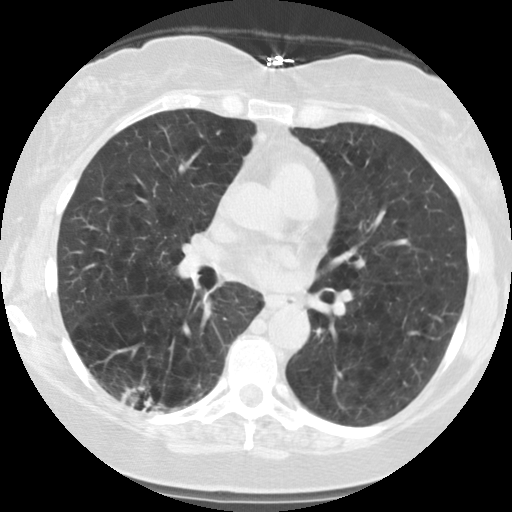
Chest CT (low-dose screening protocol), one axial image. Second annual screen. Lung window (W 1500 / L -600 HU). 2.5 mm slice thickness. Female, age 59 years at enrolment. Current smoker at enrolment.
Expert-annotated lung lesion, bounding box [x1, y1, x2, y2] px = [106, 362, 185, 426]. The screening reader recorded 2 non-calcified nodules or masses ≥4 mm on this exam; which of them this box marks is not recorded. Official screen result: positive, other. Later outcome: lung cancer diagnosed 63 days after this screen — squamous cell carcinoma, NOS, right lower lobe, poorly differentiated (G3), stage IB (AJCC 6th edition), 30 mm at pathology.